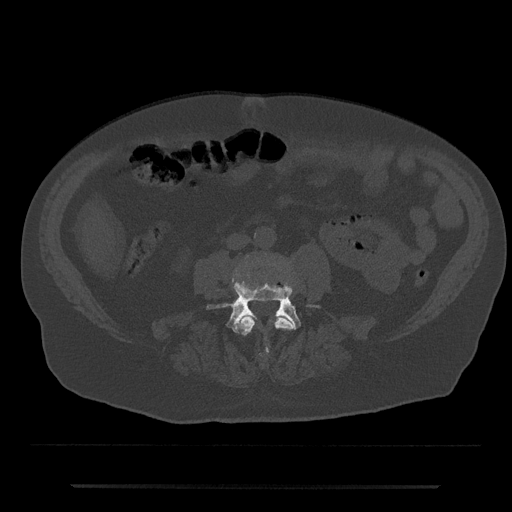
CT including the spine, one axial slice. Position 370 of 797 along the scan axis. Reconstruction kernel Br40s/3. 120 kVp. Bone window (W 1800 / L 400 HU). 0.5 mm slice thickness. 512 × 512 image matrix, field of view 434 × 434 mm. Patient: male, 80 years. Case-level facts recorded for this patient, not image findings: primary cancer: prostate; vertebrae with lytic lesions (as recorded): L1, T11.
Outlined on this slice (semi-automatic segmentation, software-assisted and operator-edited):
- L3 vertebra: bounding box (x1, y1, x2, y2) in pixels: (236, 315, 294, 355)
- L4 vertebra: (206, 281, 319, 332)